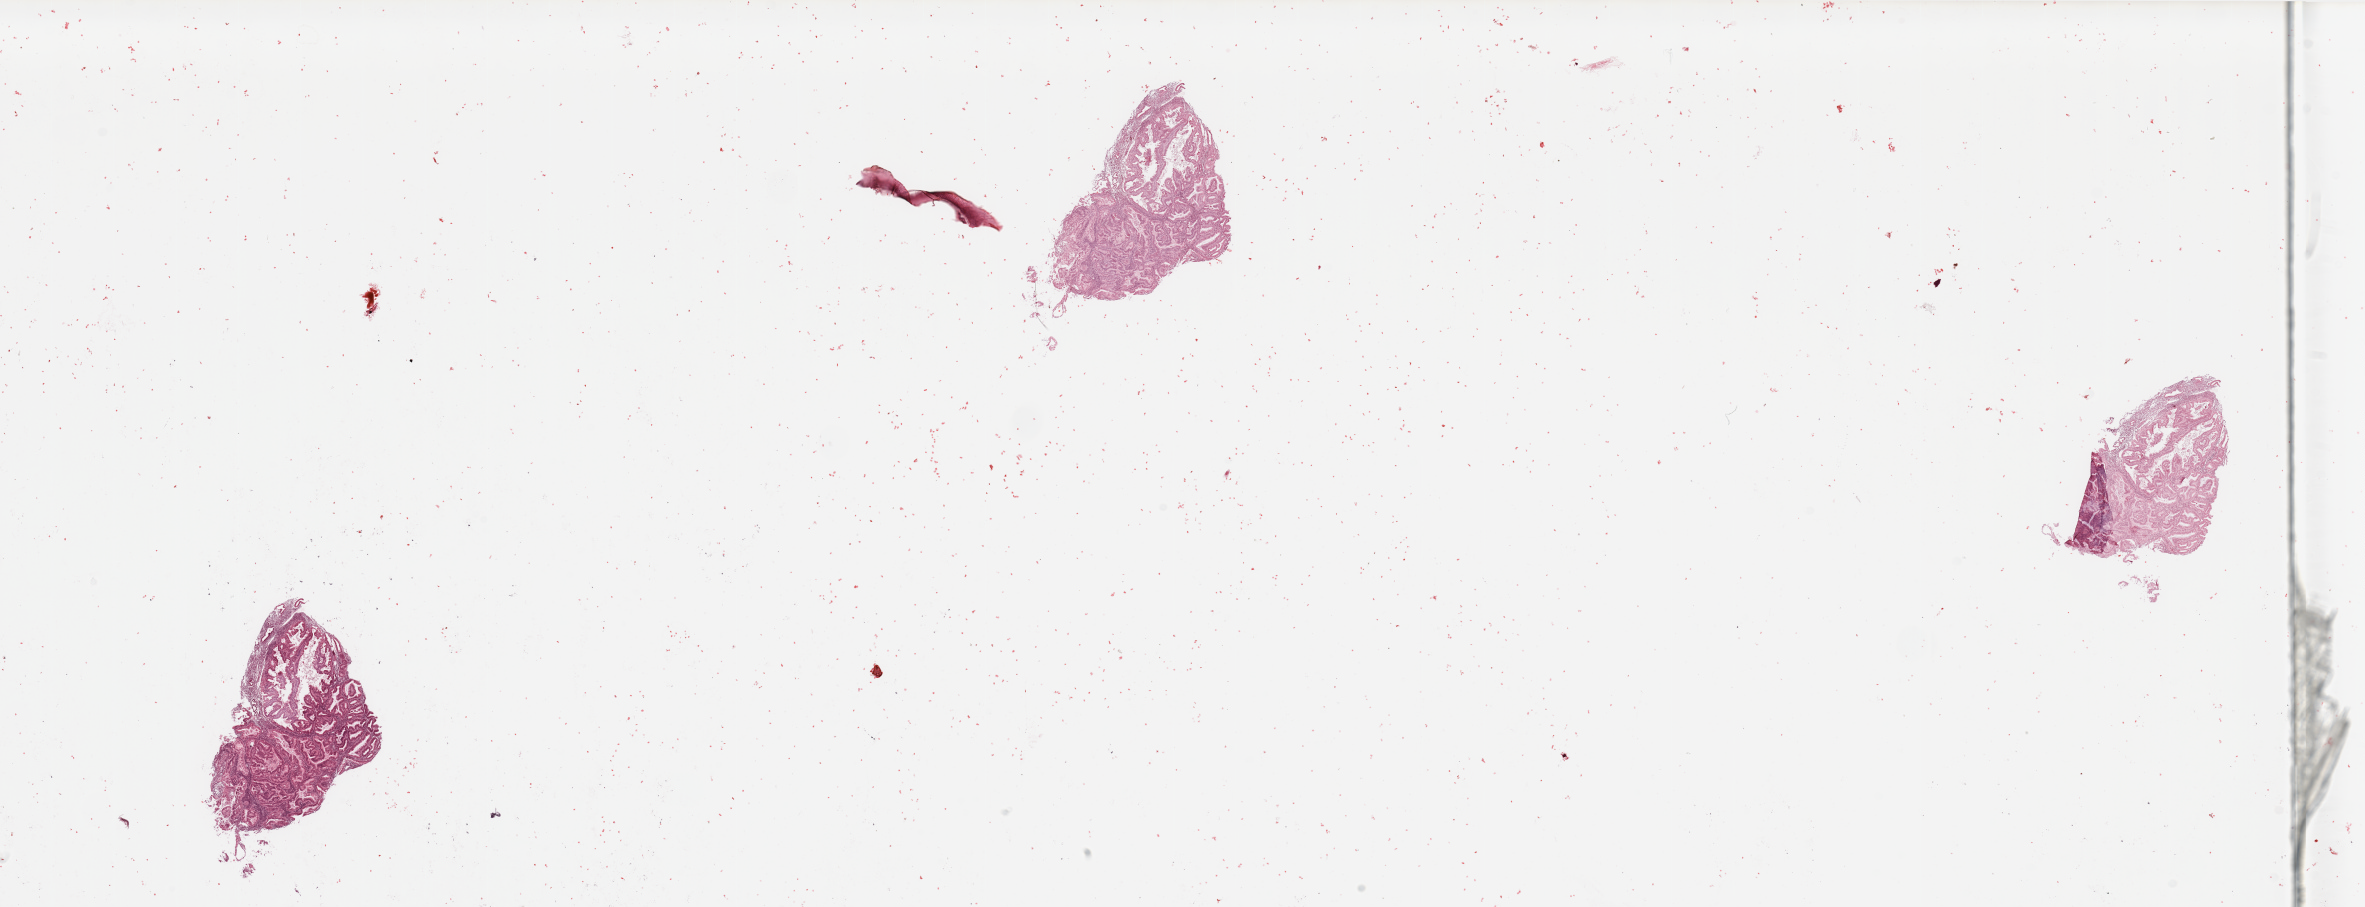
Whole-slide histology image, H&E-stained, whole scanned area (about 37.4 x 14.3 mm, from a 20x scan) shown as a low-resolution overview, uterus, tumour tissue. 67-year-old female patient. Histologic grade: G1 (well differentiated).
AJCC pathologic stage: I. Histologic diagnosis: Endometrioid adenocarcinoma, NOS. Primary tumour site (as recorded): posterior endometrium.